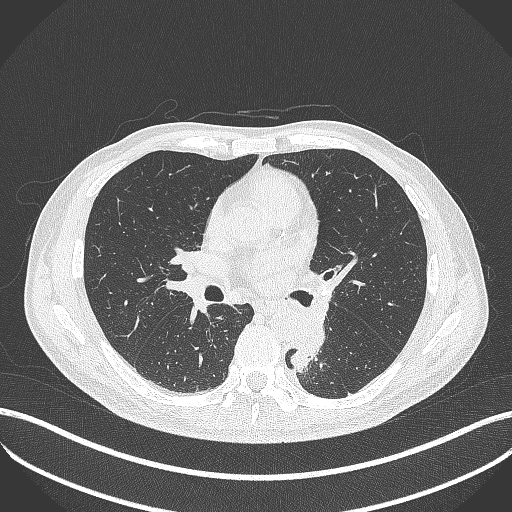
Chest CT, one axial slice; slice 220 of 451 in the series (ordered by position); lung window (W 1500 / L -600 HU); 1 mm slice thickness; 512 × 512 image matrix, field of view 400 × 400 mm. Male patient, age 72 years. Case-level facts recorded for this patient, not image findings: clinical TNM (as recorded): T2b N0 M1.
Annotated regions visible in this slice (bounding box drawn by a radiologist):
- lung tumour (recorded histology: adenocarcinoma): bounding box <285,328,330,374> (left, top, right, bottom; pixels)